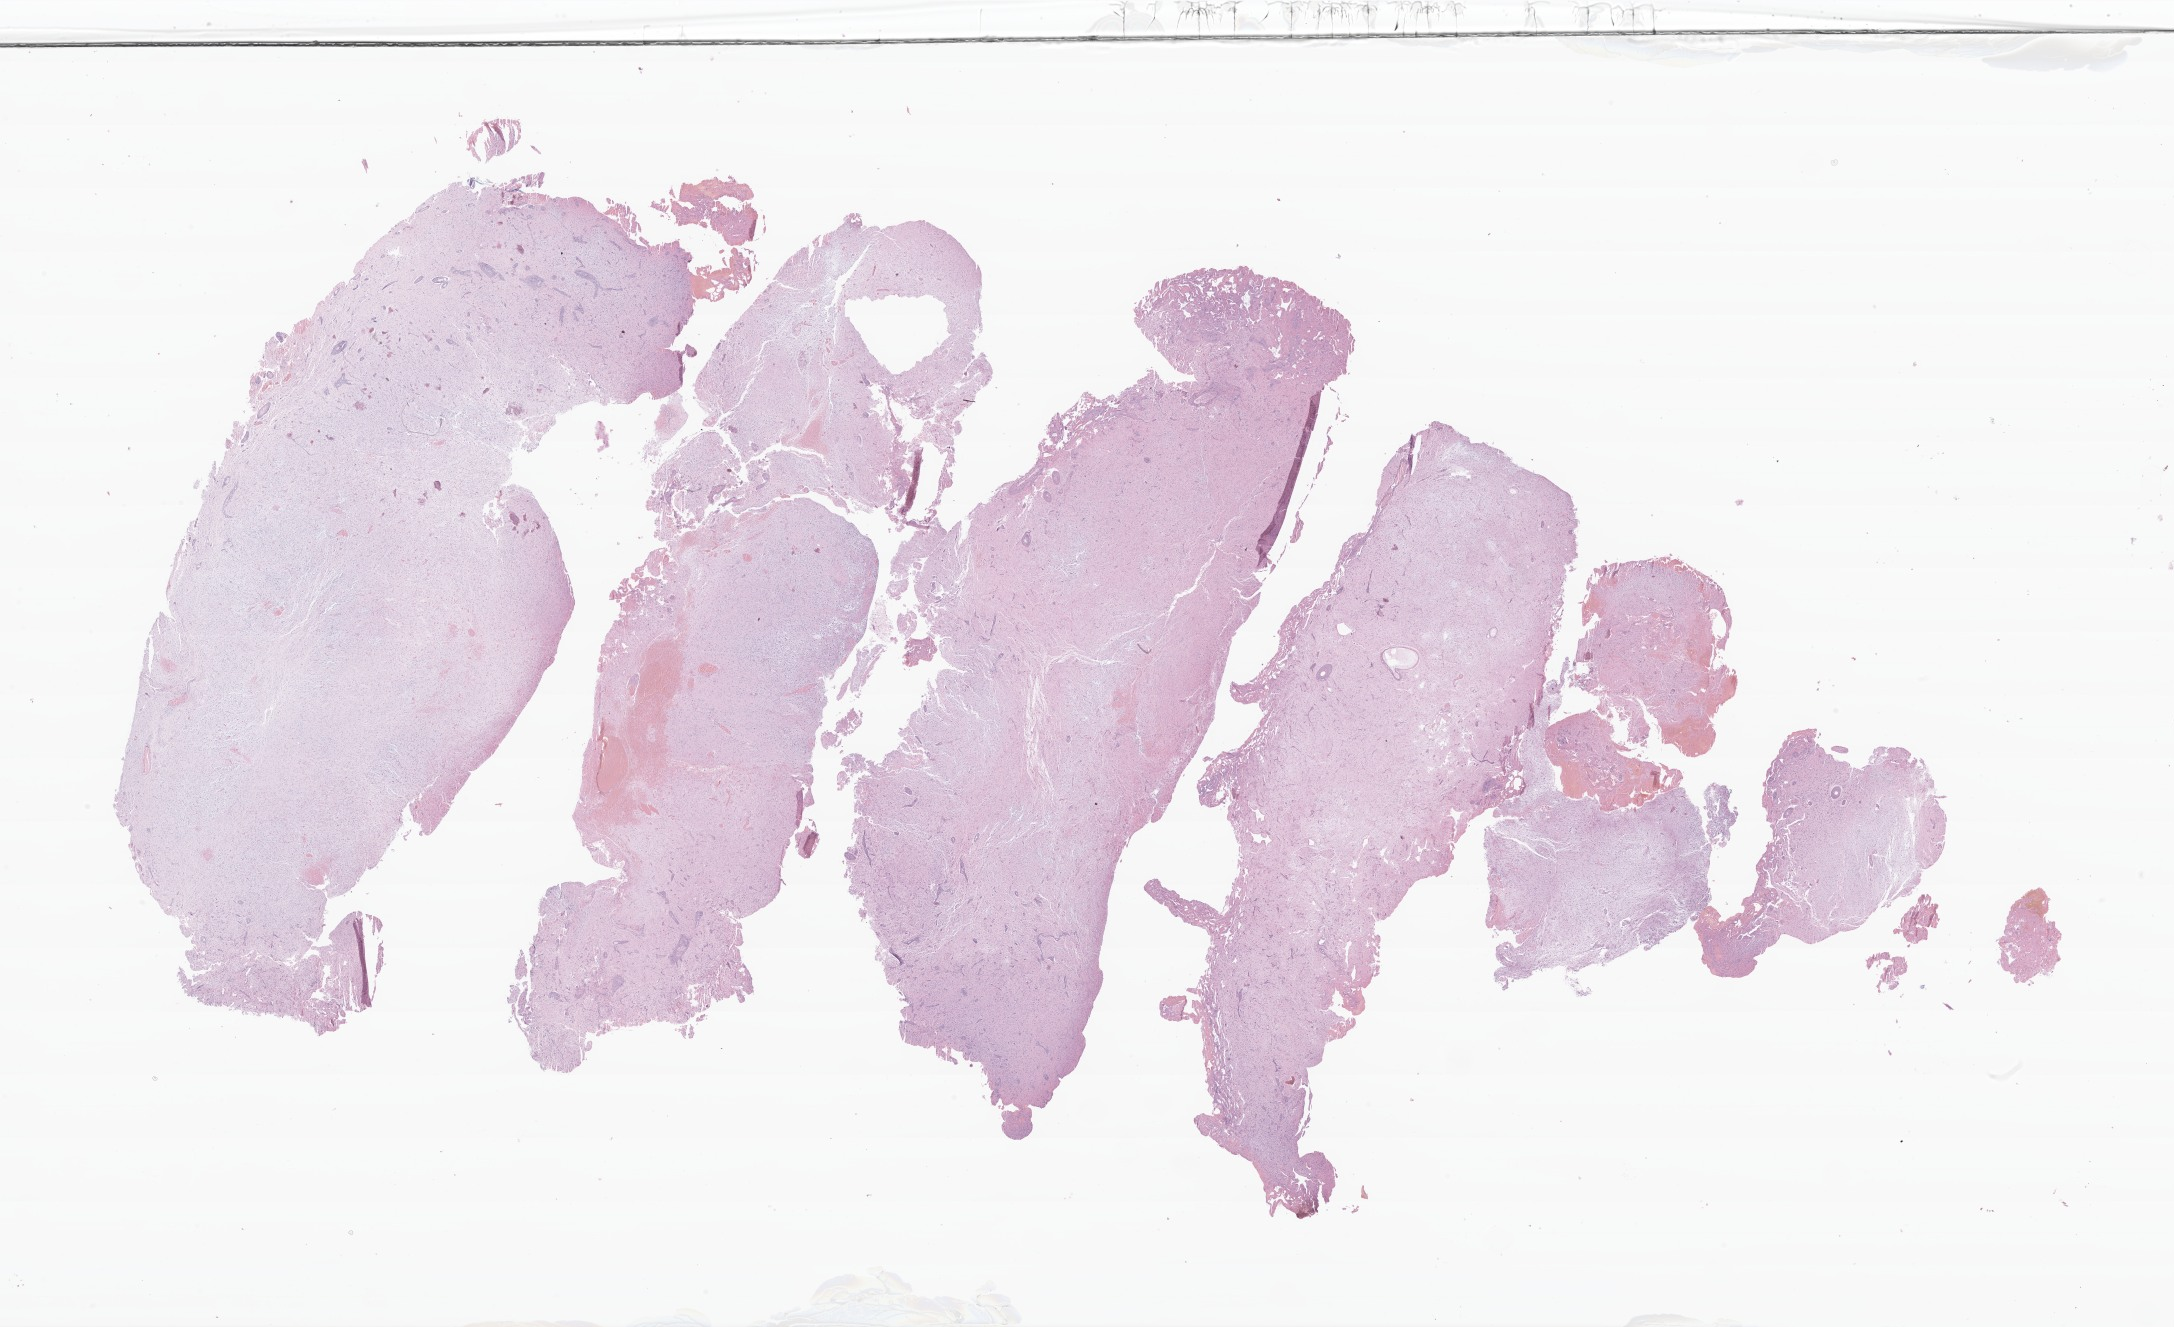
Haematoxylin and eosin whole-slide image of tumor tissue from the brain, a low-resolution overview of the entire scanned area, about 36.6 x 22.3 mm. Formalin-fixed, paraffin-embedded (FFPE) tissue. Patient male; age 197 months.
Diagnosis: Pilocytic astrocytoma.